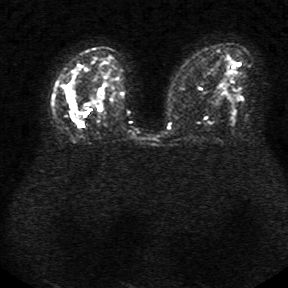
Breast MRI, one axial slice; position 16 of 34 along the scan axis; diffusion-weighted series; image 2 of 4 stored at this slice position (different b-values; order by instance number); 1.5 T; 5 mm slice thickness; 288 × 288 image matrix. Female patient.
Annotated regions visible in this slice (expert manual segmentation):
- tumour on diffusion-weighted imaging: bounding box (x1, y1, x2, y2) in pixels: (83, 83, 106, 119)